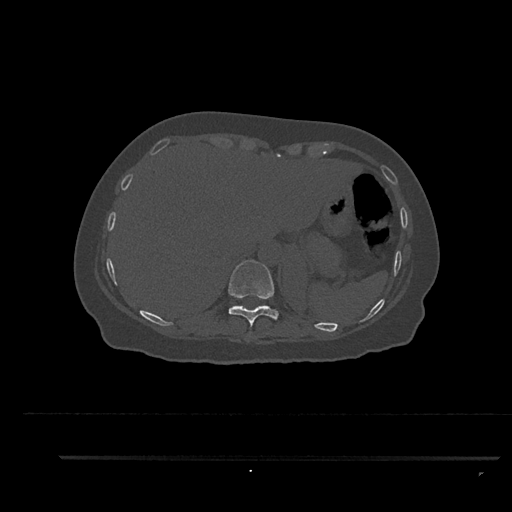
CT including the spine, one axial slice. Bone window (W 1800 / L 400 HU). 0.5 mm slice thickness. 512 × 512 image matrix, field of view 408 × 408 mm. Female patient, age 44 years. From the clinical record (not read from this slice): primary cancer: renal.
Structures marked on this image (semi-automatically segmented with operator editing):
- T10 vertebra: bounding box (x1, y1, x2, y2) in pixels: (228, 260, 279, 333)